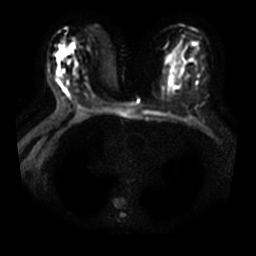
Breast MRI, one axial slice. Slice 19 of 33 in the series (ordered by position). Diffusion-weighted series; image 2 of 4 stored at this slice position (different b-values; order by instance number). 3 T. 256 × 256 image matrix, field of view 350 × 350 mm. Female patient.
Outlined on this slice (expert manual segmentation):
- tumour on diffusion-weighted imaging: bounding box <57,47,64,61> (left, top, right, bottom; pixels)